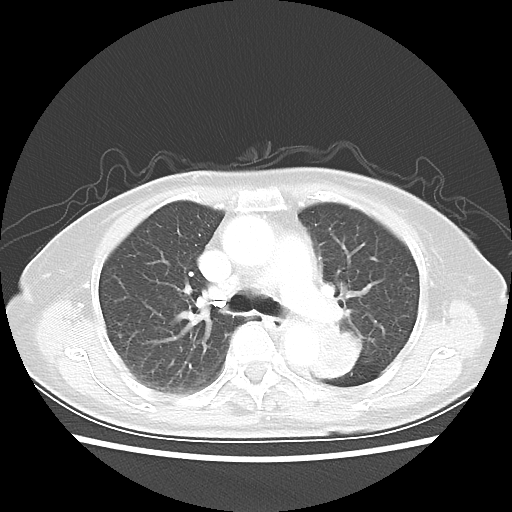
Chest CT, one axial slice; slice 32 of 50 in the series (ordered by position); reconstruction kernel LUNG; lung window (W 1500 / L -600 HU); 512 × 512 image matrix. Female patient, age 81 years. Case-level facts recorded for this patient, not image findings: clinical TNM (as recorded): T2 N0 M1a.
Outlined on this slice (bounding box drawn by a radiologist):
- lung tumour (recorded histology: squamous cell carcinoma): bounding box [x1, y1, x2, y2] px = [307, 315, 370, 385]